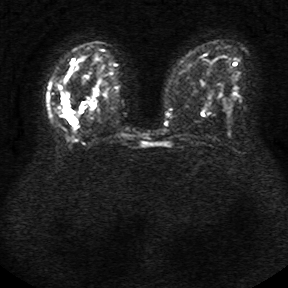
Breast MRI, one axial slice. Position 16 of 34 along the scan axis. Diffusion-weighted series; image 2 of 4 stored at this slice position (different b-values; order by instance number). 1.5 T. 5 mm slice thickness. 288 × 288 image matrix. Female patient.
Structures marked on this image (outlined manually by an expert reader):
- tumour on diffusion-weighted imaging: bounding box <79,88,100,114> (left, top, right, bottom; pixels)